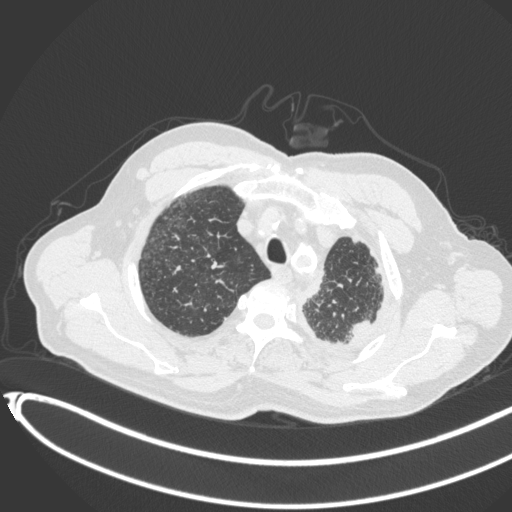
Chest CT, one axial slice. Slice 362 of 451 in the series (ordered by position). Reconstruction kernel B31f. Lung window (W 1500 / L -600 HU). 512 × 512 image matrix, field of view 400 × 400 mm. Patient: male, 78 years. From the clinical record (not read from this slice): clinical TNM (as recorded): T1c N0 M1.
Structures marked on this image (rectangle marked by the reading radiologist):
- lung tumour (recorded histology: adenocarcinoma): box from (x=349, y=317) to (x=373, y=340) px